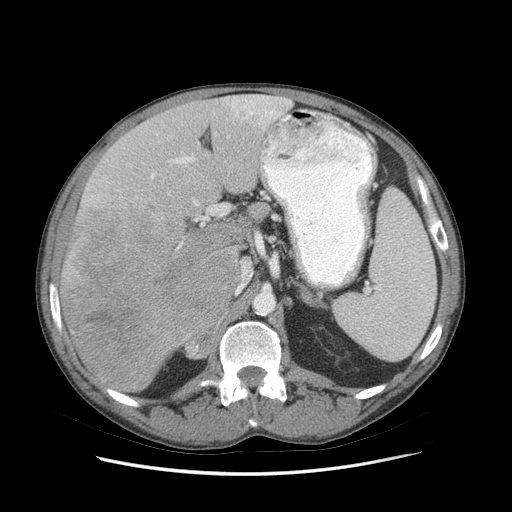
Contrast-enhanced abdominal CT (liver protocol), one axial slice; soft-tissue window (W 400 / L 40 HU); 2.5 mm slice thickness; 512 × 512 image matrix, field of view 380 × 380 mm. Case-level facts recorded for this patient, not image findings: diagnosis: hepatocellular carcinoma (patient treated with transarterial chemoembolisation; whether this scan precedes or follows treatment is not stated here); TNM stage (as recorded): Stage-IIIB.
Structures marked on this image (semi-automatically segmented with operator editing):
- liver parenchyma outside the tumour (the mass and vessels are separate outlines, so this box may not span the whole liver): bounding box (x1, y1, x2, y2) in pixels: (60, 94, 290, 392)
- mass: (58, 207, 240, 390)
- liver vessels: (151, 96, 289, 221)